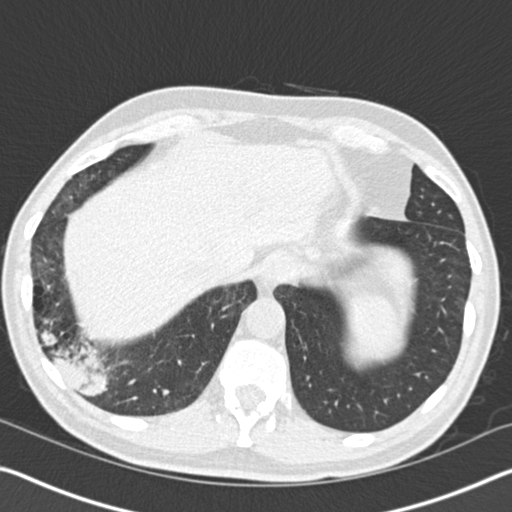
Axial slice from a low-dose chest CT screening exam. First (baseline) screen. Lung window (W 1500 / L -600 HU). 2 mm slice thickness. Standard (soft-tissue) reconstruction kernel (B30f). 512 × 512 image matrix. Male, age 61 years at enrolment. Current smoker at enrolment.
Expert reader's lesion annotation, box from (x=8, y=272) to (x=136, y=413) px. Screening reader's record for this exam (one nodule recorded; not confirmed to be the boxed lesion): non-calcified nodule or mass ≥4 mm, right lower lobe, 52 × 36 mm, spiculated (stellate) margins, soft tissue attenuation. Later outcome: lung cancer diagnosed 392 days after this screen (after the second annual screen) — bronchiolo-alveolar adenocarcinoma, NOS, right lower lobe, moderately differentiated (G2), stage IIIB (AJCC 6th edition), 90 mm at pathology.